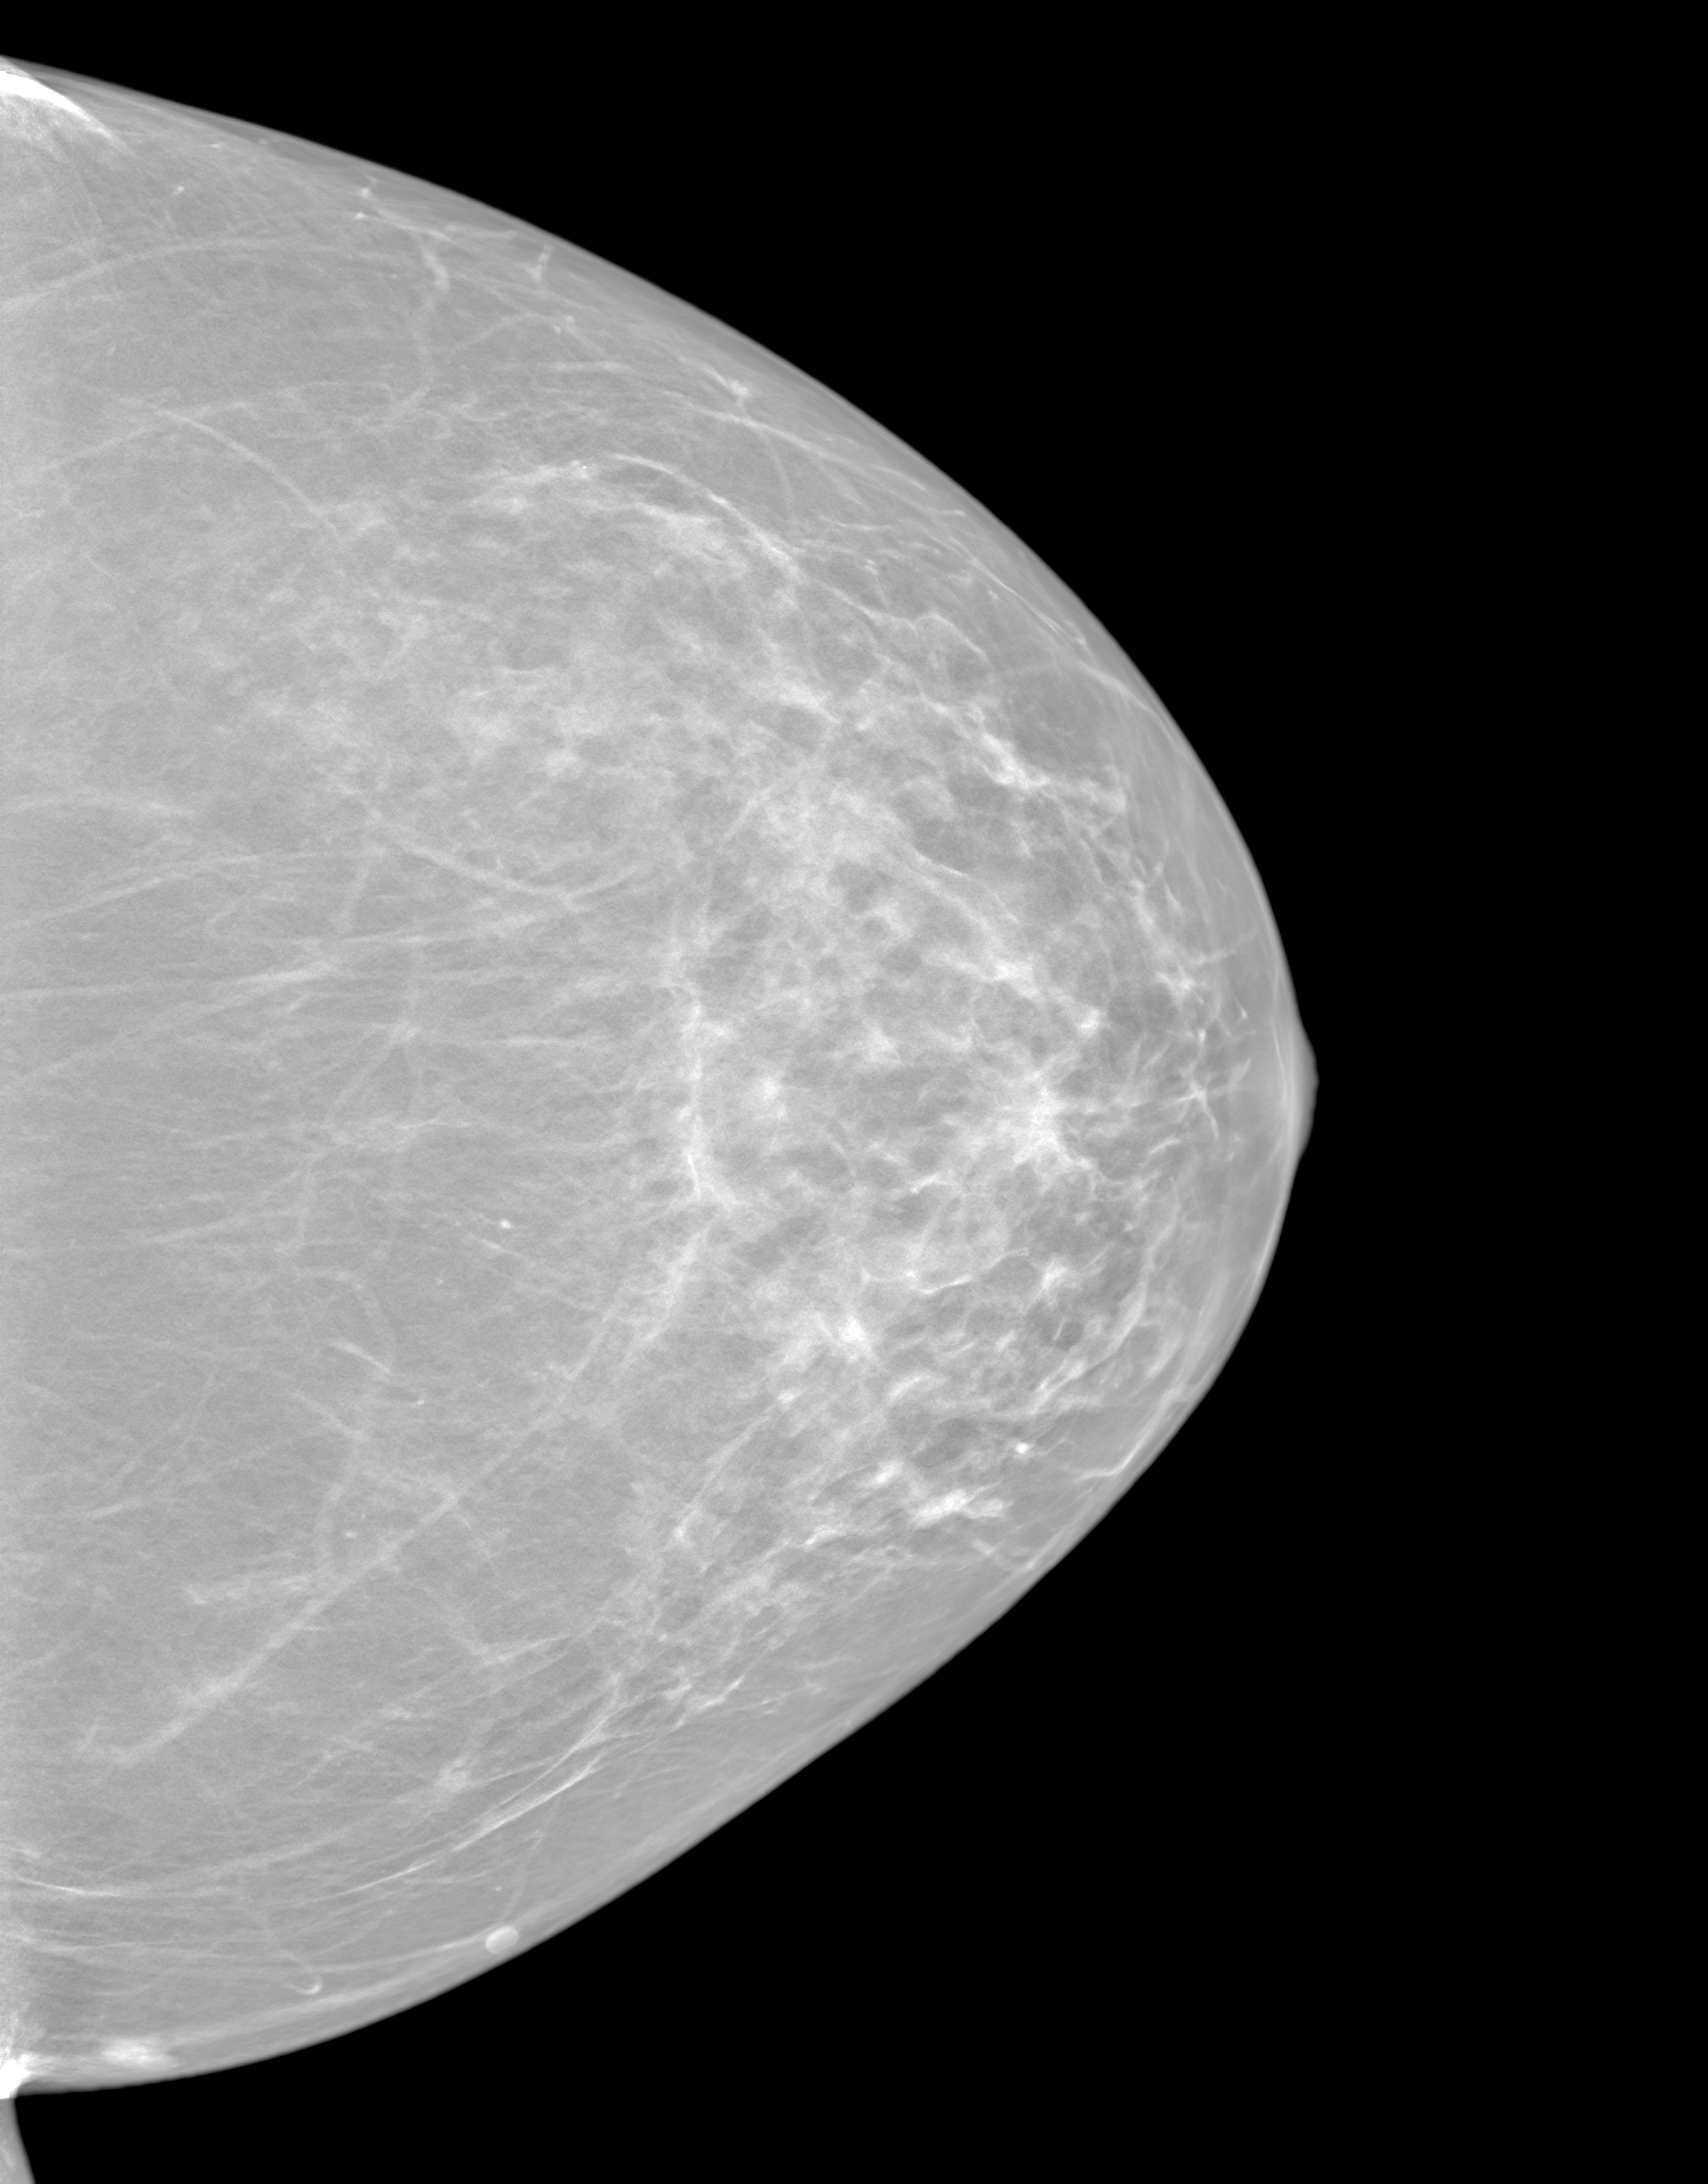
Annual screening mammography examination; system: SenoIris_1SP1.1(421). Female patient, age 58 years.
Image type: synthesized 2-D view from tomosynthesis. Breast: left. Projection: CC view.